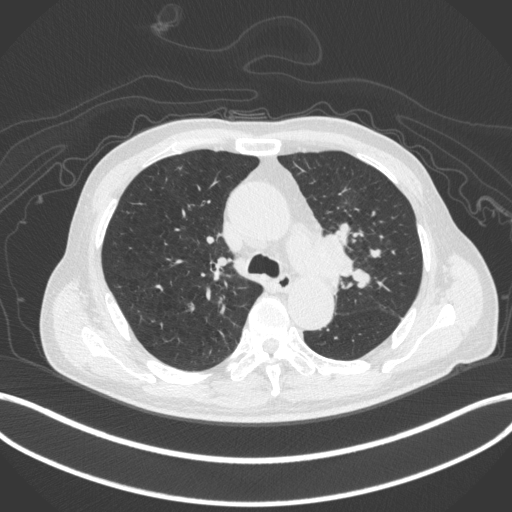
Chest CT, one axial slice; position 294 of 420 along the scan axis; reconstruction kernel B31f; lung window (W 1500 / L -600 HU); 512 × 512 image matrix, field of view 400 × 400 mm. Patient: male, 77 years. Case-level facts recorded for this patient, not image findings: clinical TNM (as recorded): T3 N1 M0.
Annotated regions visible in this slice (rectangle marked by the reading radiologist):
- lung tumour (recorded histology: adenocarcinoma): bounding box (x1, y1, x2, y2) in pixels: (299, 222, 360, 283)